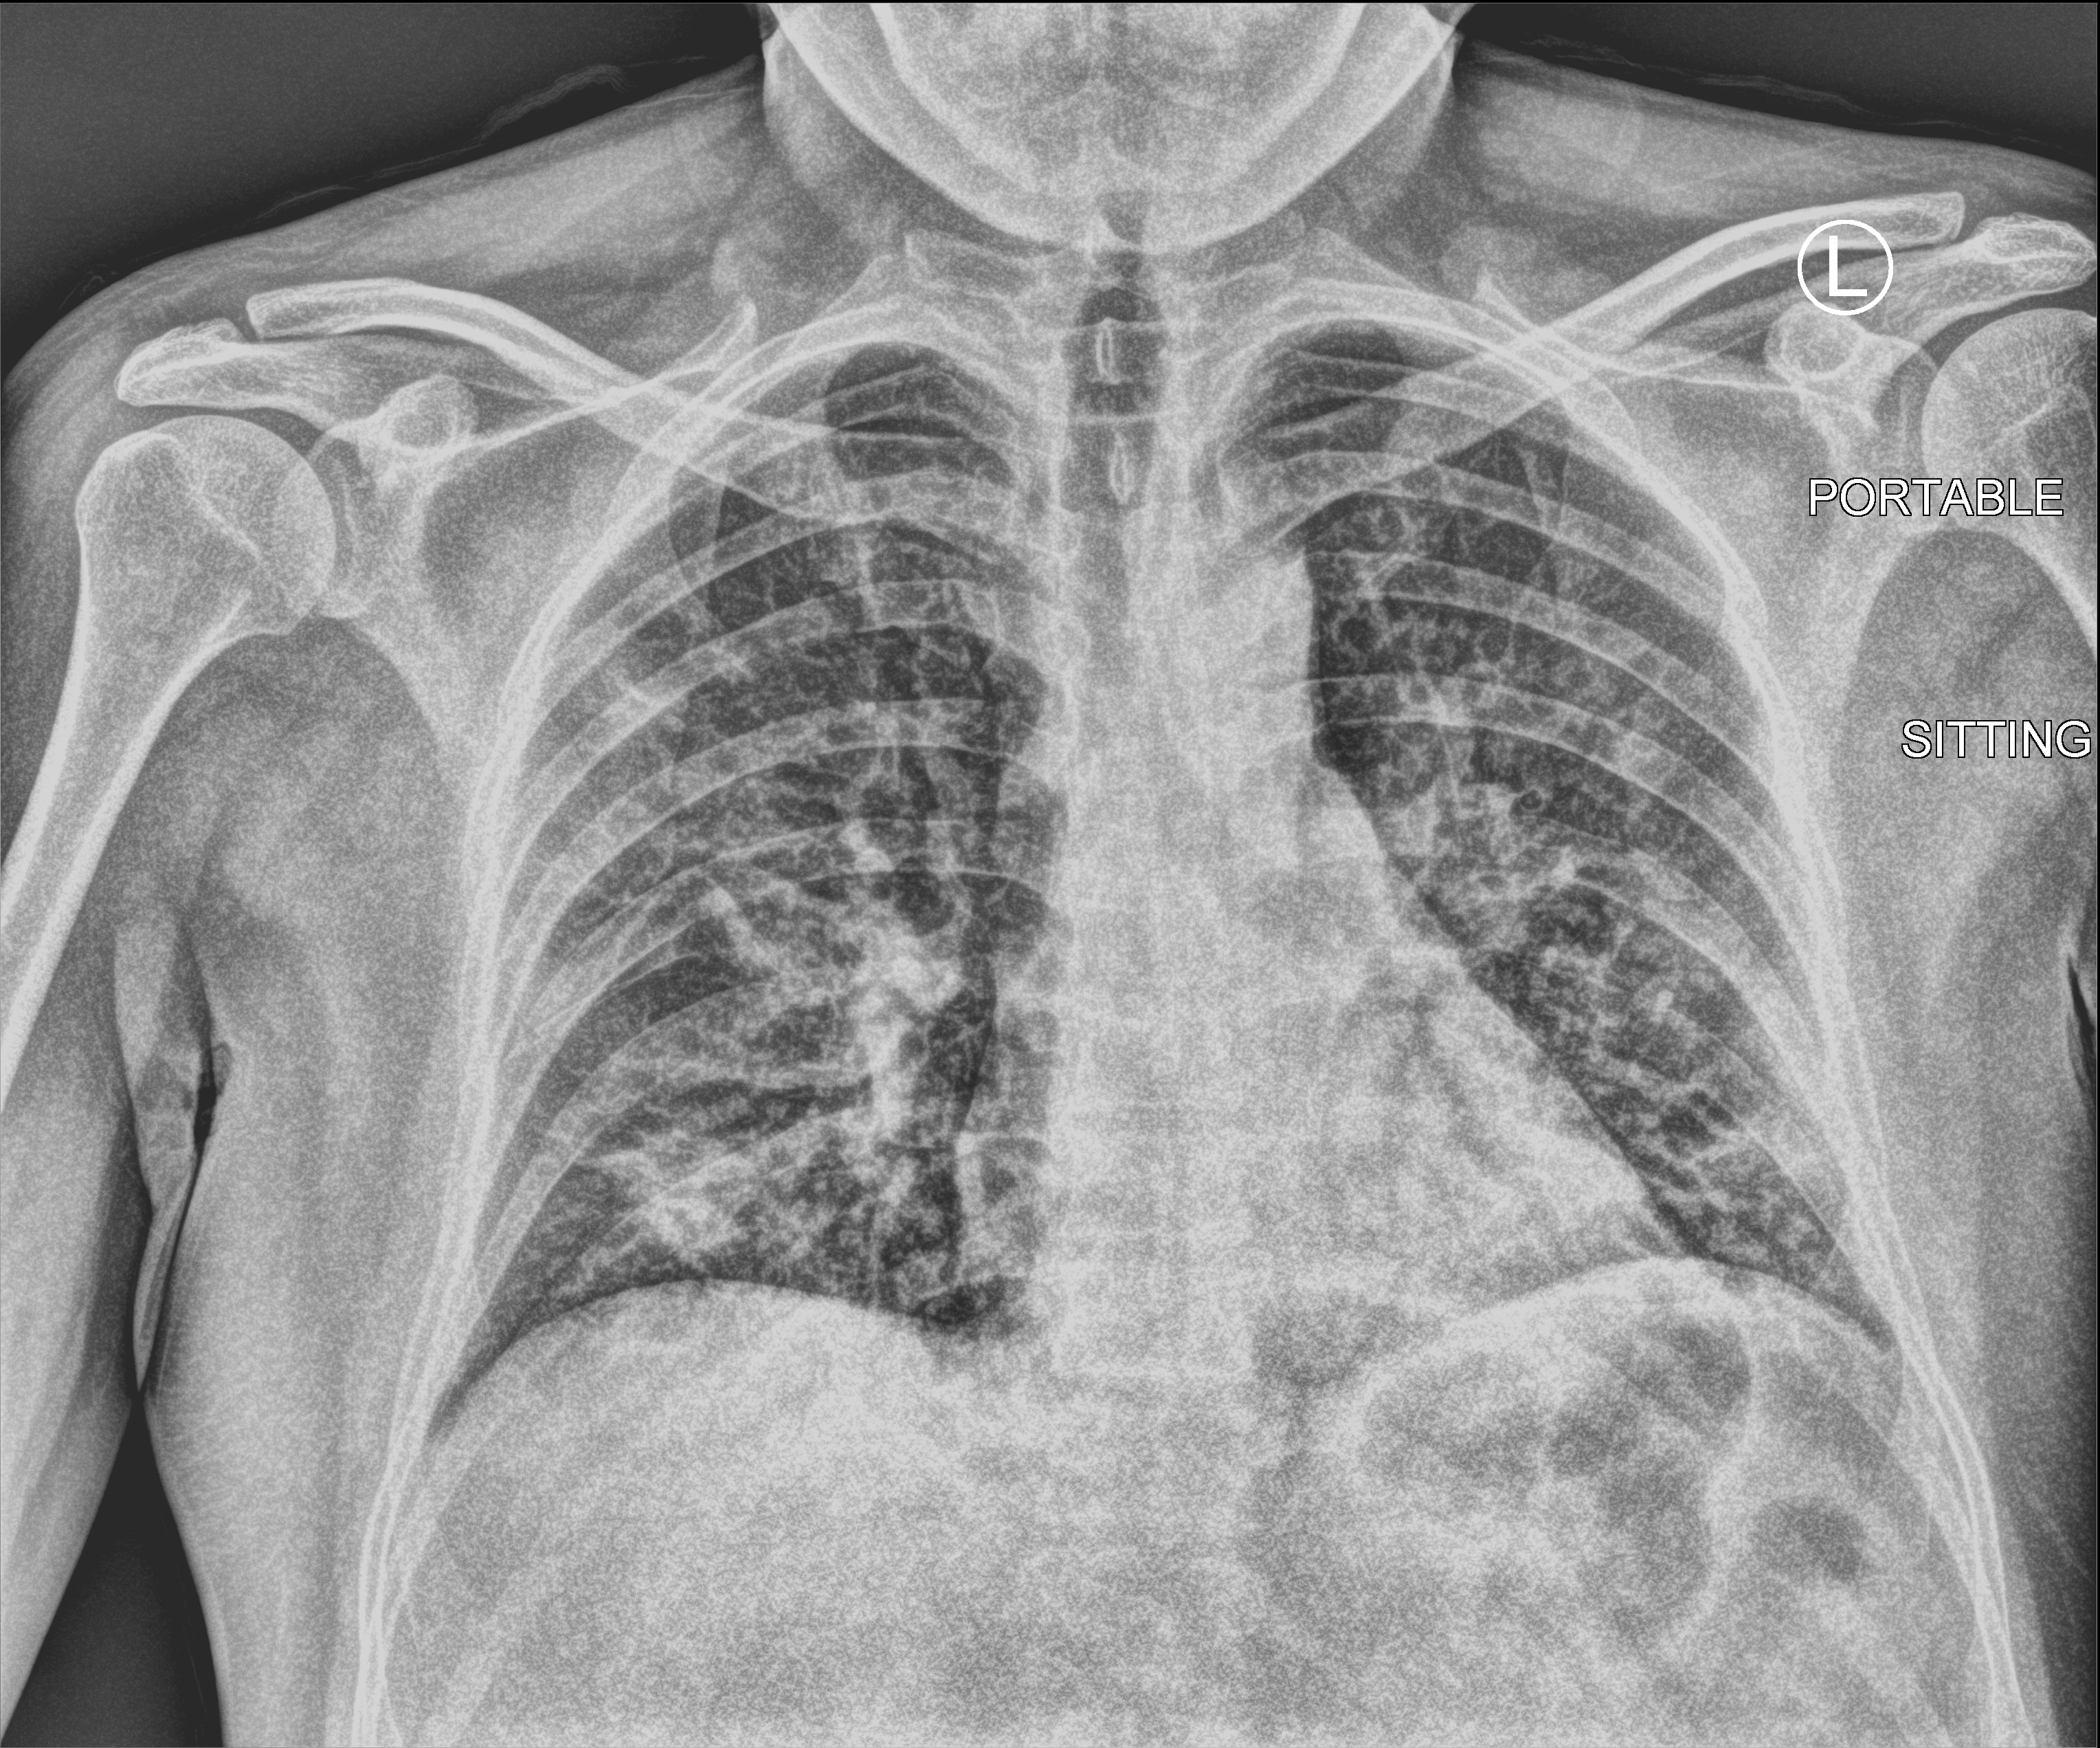
Chest X-ray (portable), anteroposterior (AP) projection. Male patient hospitalised with COVID-19, age 18–59 years.
From the hospital-stay record, not from the radiograph (when in the stay this image was taken is not recorded): mechanically ventilated during this hospital stay: no; diabetes (admission record): no; admitted to intensive care during this hospital stay: no.